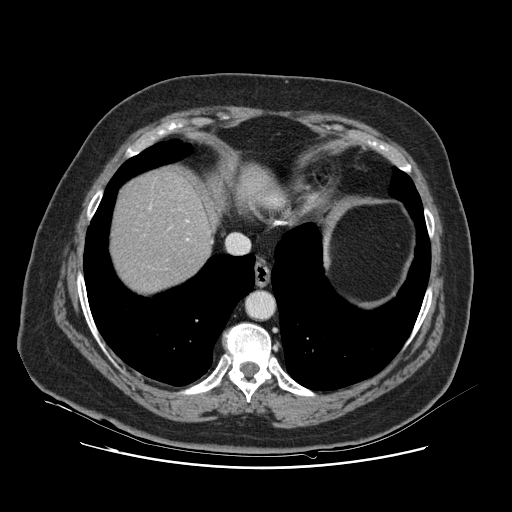
Contrast-enhanced abdominal CT, one axial slice; slice 109 of 132 in the series (ordered by position); 120 kVp; soft-tissue window (W 400 / L 40 HU); 2.5 mm slice thickness; 512 × 512 image matrix, field of view 391 × 391 mm. Female patient, age 73 years. Case-level facts recorded for this patient, not image findings: diagnosis: colorectal cancer liver metastases, imaged before liver resection; multiple liver metastases: no; largest metastasis: 7 cm; chemotherapy before resection: yes.
Structures marked on this image (manually delineated by an expert):
- hepatic veins: bounding box <150,206,189,240> (left, top, right, bottom; pixels)
- liver: <112,173,211,293>
- planned liver remnant (the part of the liver to remain after resection): <112,173,210,293>